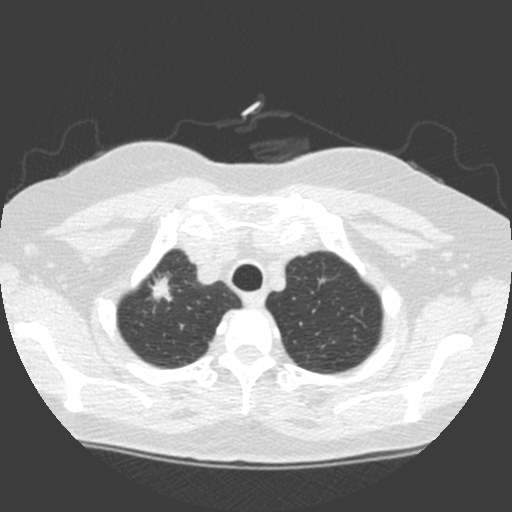
Low-dose screening chest CT, axial slice. Baseline annual screen. Lung window (W 1500 / L -600 HU). 2 mm slice thickness. 120 kVp. Female, age 63 years at enrolment.
Expert-annotated lung lesion, bounding box (x1, y1, x2, y2) in pixels: (135, 268, 182, 308). Screening reader's record for this exam (one nodule recorded; not confirmed to be the boxed lesion): non-calcified nodule or mass ≥4 mm, right upper lobe, 11 × 11 mm, spiculated (stellate) margins, soft tissue attenuation. Later outcome: lung cancer diagnosed 6 days after this screen — adenocarcinoma, NOS, right upper lobe, poorly differentiated (G3), stage IA (AJCC 6th edition), 17 mm at pathology.